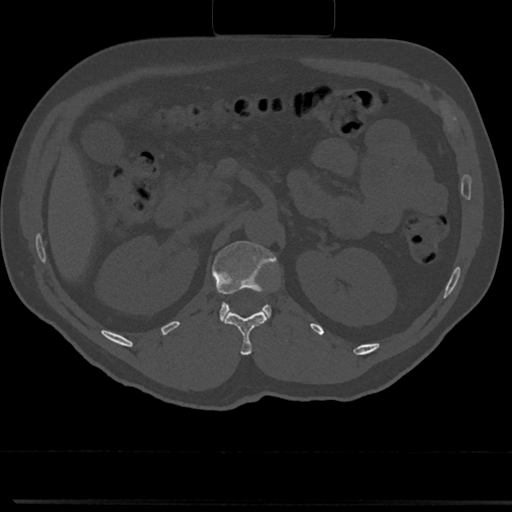
CT including the spine, one axial slice. Slice 112 of 817 in the series (ordered by position). Reconstruction kernel Br40s/3. Bone window (W 1800 / L 400 HU). 512 × 512 image matrix. Male patient, age 61 years. From the clinical record (not read from this slice): primary cancer: prostate.
Outlined on this slice (semi-automatic segmentation, software-assisted and operator-edited):
- L1 vertebra: bounding box <213,240,278,326> (left, top, right, bottom; pixels)
- T12 vertebra: <223,311,268,354>